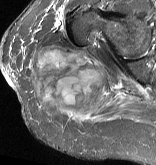
MRI of an extremity soft-tissue mass, one axial slice. Slice 36 of 57 in the series (ordered by position). STIR. MR volume resampled by the dataset authors to the PET/CT grid (not the native acquisition matrix). 156 × 165 image matrix. Female patient. Case-level facts recorded for this patient, not image findings: histological type: epithelioid sarcoma with vascular differentiation; site of the primary tumour: right buttock.
Structures marked on this image (expert contour drawn on MRI and transferred to this co-registered scan by the dataset authors):
- gross tumour volume (mass): bounding box [x1, y1, x2, y2] px = [29, 48, 114, 111]